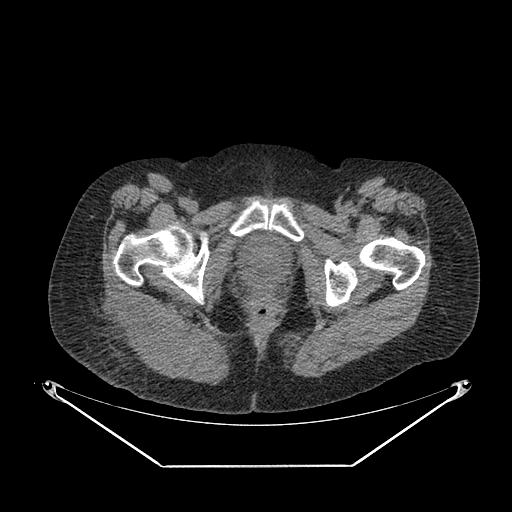
CT of an extremity soft-tissue mass (from a PET/CT study), one axial slice. Position 48 of 267 along the scan axis. 140 kVp. Soft-tissue window (W 400 / L 40 HU). 512 × 512 image matrix, field of view 500 × 500 mm. Female patient. Case-level facts recorded for this patient, not image findings: histological type: spindle cell suggestive of myxofibrosarcoma; grade: intermediate; site of the primary tumour: right buttock.
Outlined on this slice (expert contour drawn on MRI and transferred to this co-registered scan by the dataset authors):
- gross tumour volume (mass): box from (x=105, y=299) to (x=184, y=359) px